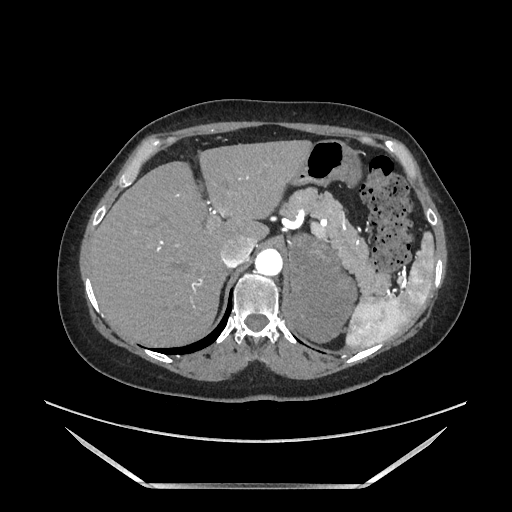
Contrast-enhanced abdominal CT, one axial slice. Position 134 of 205 along the scan axis. Soft-tissue window (W 400 / L 40 HU). 1.25 mm slice thickness. 512 × 512 image matrix. Female patient. Case-level facts recorded for this patient, not image findings: diagnosis: adrenocortical carcinoma; tumour side: left adrenal; tumour size at pathology: 12.5 cm; Ki-67 index: 39 %; stage (as recorded): 3.
Annotated regions visible in this slice (semi-automatically segmented with operator editing):
- mass: box from (x=290, y=236) to (x=356, y=342) px